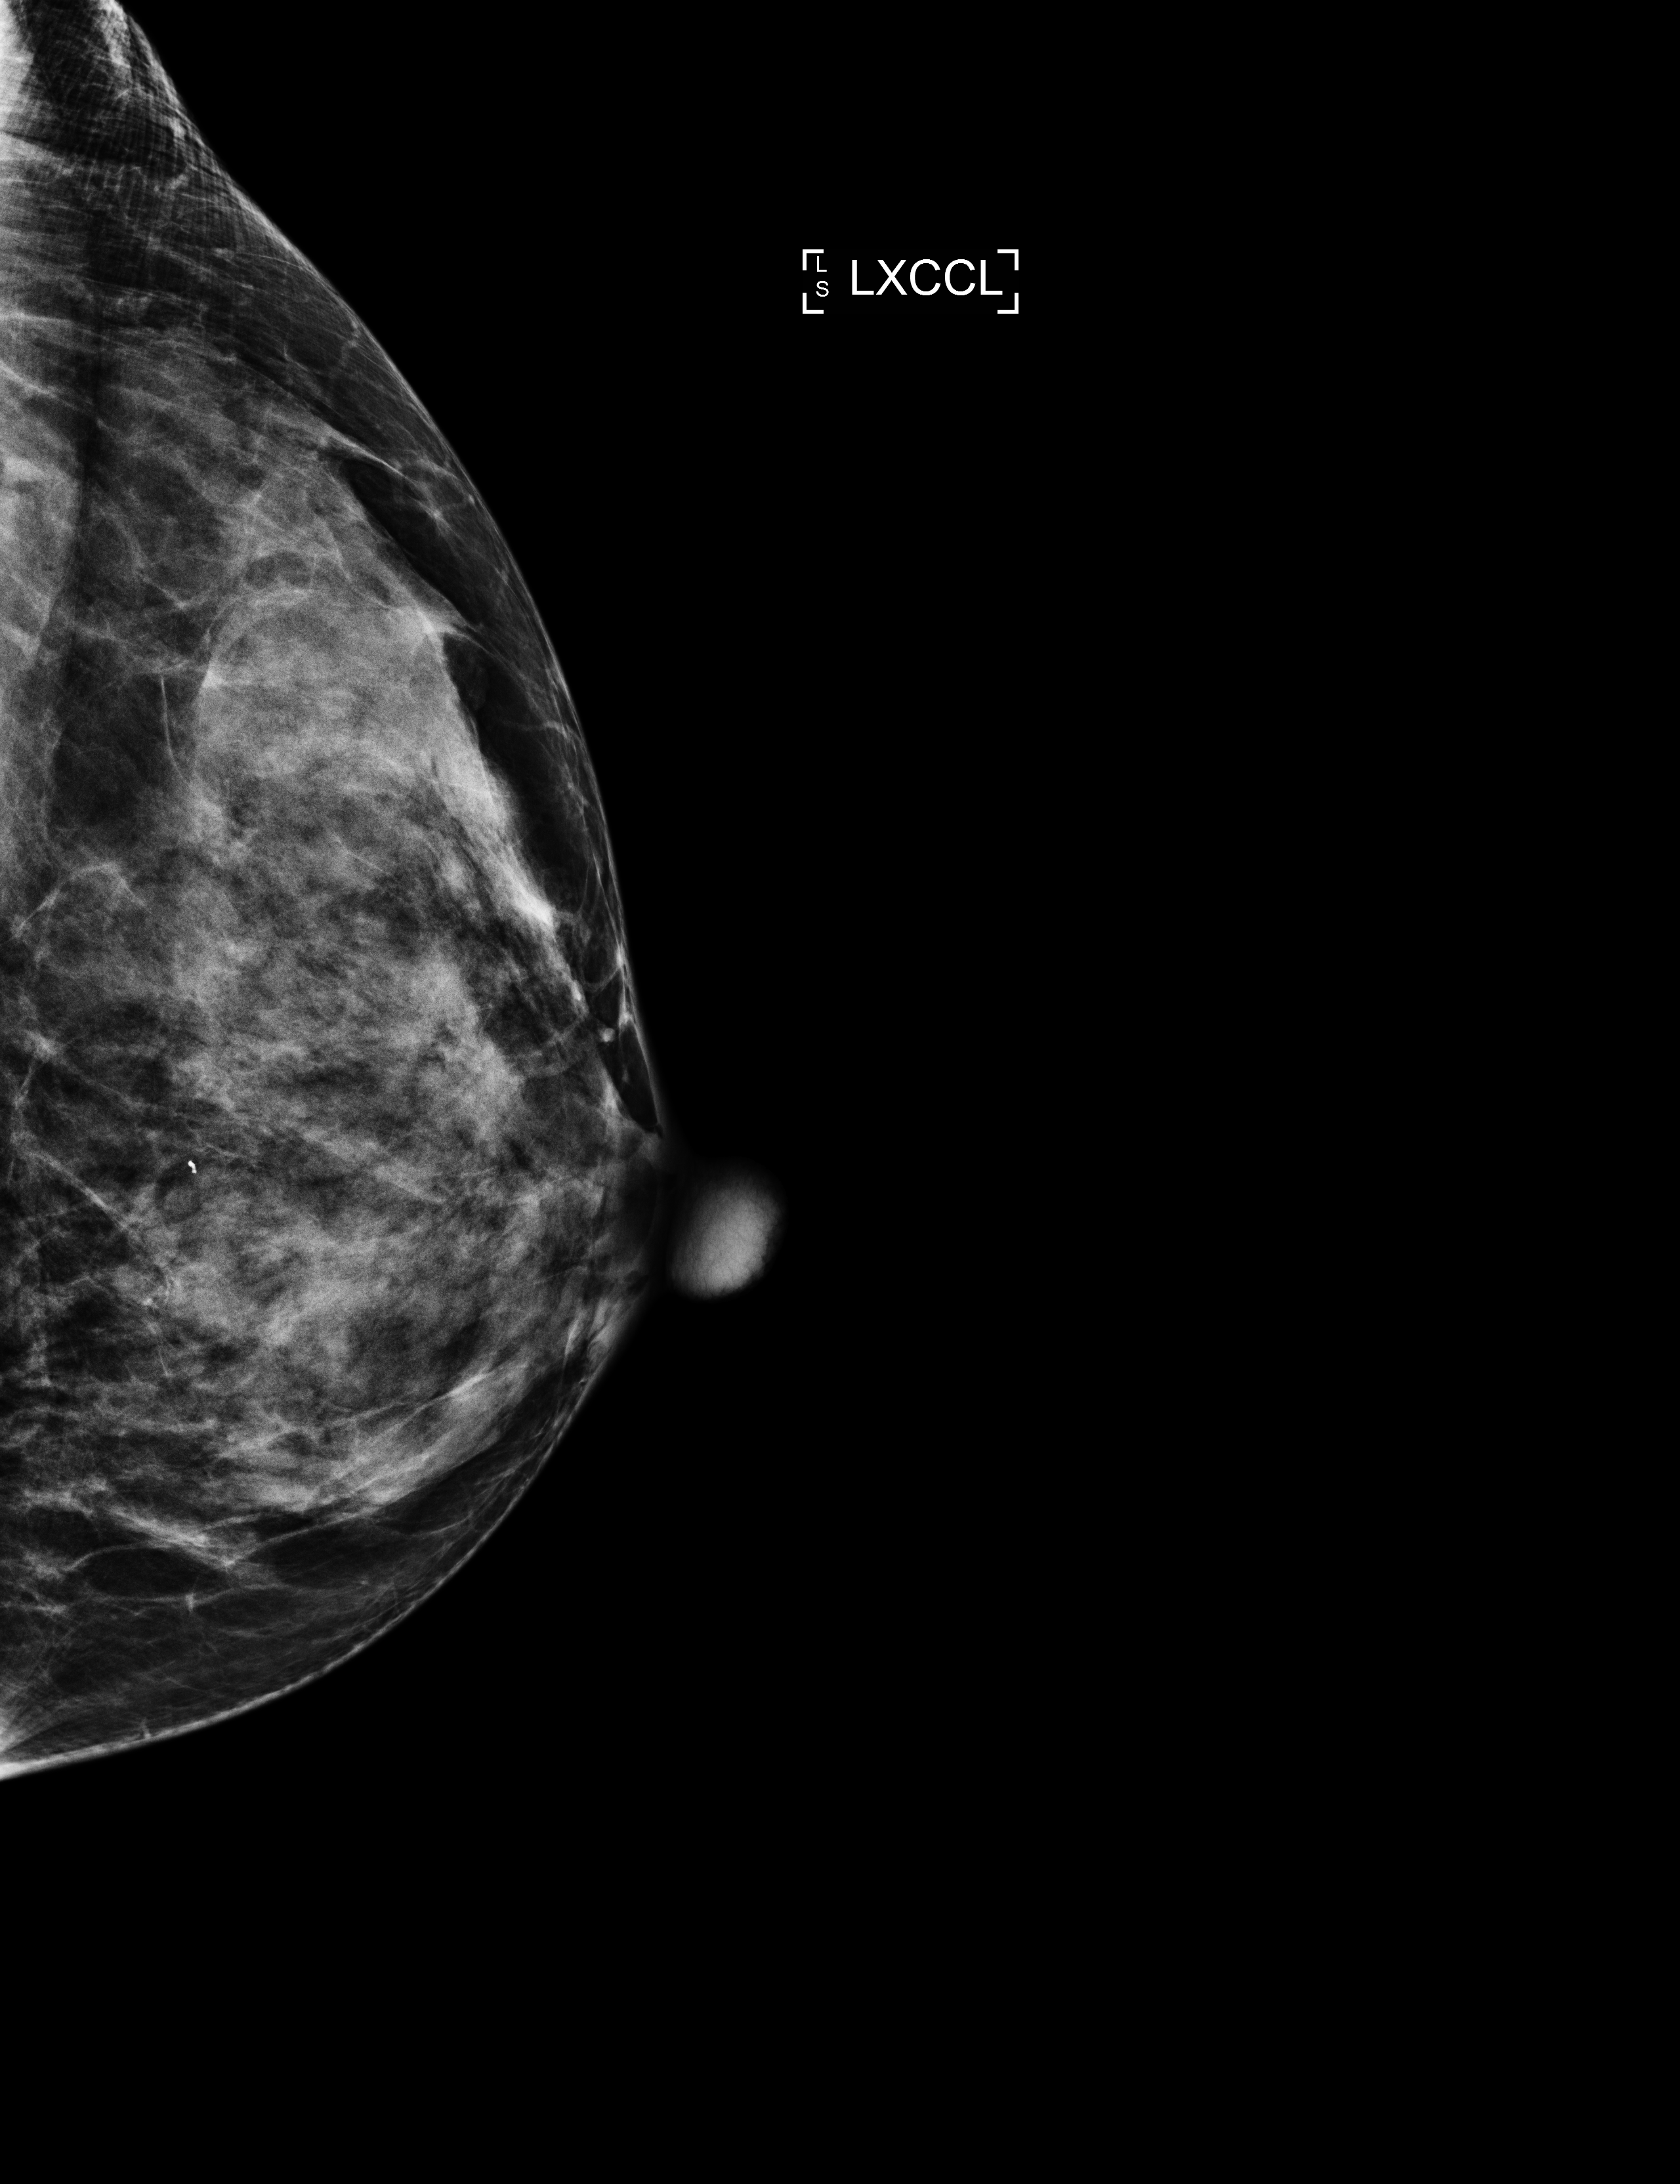
Screening examination, system: Selenia Dimensions. Patient: female, 68 years.
Image type: full-field digital mammogram. Breast: left. Projection: laterally exaggerated craniocaudal (XCCL) view.